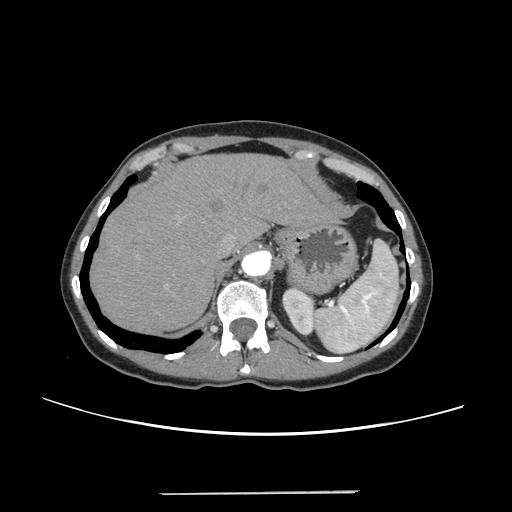
Contrast-enhanced abdominal CT, one axial slice. Intravenous contrast given. Soft-tissue window (W 400 / L 40 HU). 1.25 mm slice thickness. 512 × 512 image matrix, field of view 371 × 371 mm. Female patient, age 60 years. Case-level facts recorded for this patient, not image findings: diagnosis: colorectal cancer liver metastases, imaged before liver resection; multiple liver metastases: no.
Outlined on this slice (manually delineated by an expert):
- hepatic veins: bounding box (x1, y1, x2, y2) in pixels: (218, 236, 234, 254)
- liver: (91, 155, 329, 332)
- planned liver remnant (the part of the liver to remain after resection): (91, 155, 330, 332)
- portal vein (with intrahepatic branches): (165, 285, 169, 287)